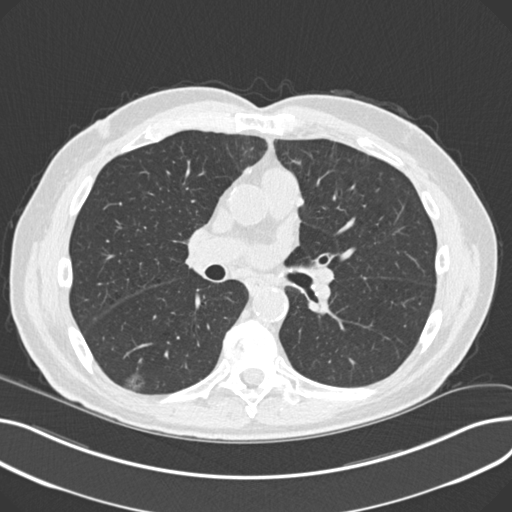
Low-dose screening chest CT, one axial slice; slice 120 of 230 in the series (ordered by position); reconstruction kernel B30f; 120 kVp; lung window (W 1500 / L -600 HU); 2 mm slice thickness; 512 × 512 image matrix.
Structures marked on this image (expert manual segmentation):
- lesion 1 (nodule, lower lobe of right lung): bounding box [x1, y1, x2, y2] px = [125, 373, 144, 391]